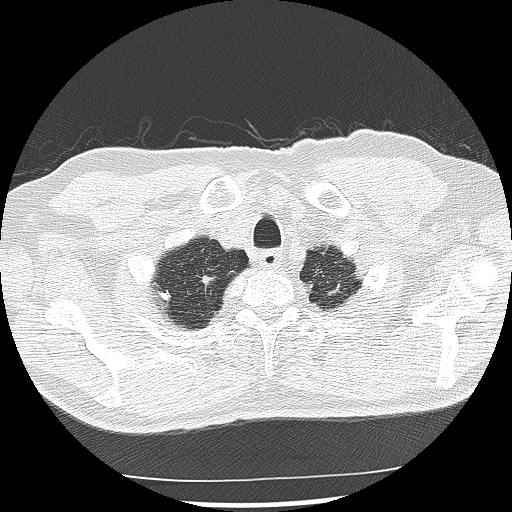
Low-dose screening chest CT, one axial slice. Slice 126 of 142 in the series (ordered by position). Reconstruction kernel LUNG. 120 kVp. Lung window (W 1500 / L -600 HU). 2.5 mm slice thickness. 512 × 512 image matrix, field of view 360 × 360 mm.
Structures marked on this image (outlined manually by an expert reader):
- lesion 3 (nodule, upper lobe of right lung): bounding box (x1, y1, x2, y2) in pixels: (201, 275, 217, 291)